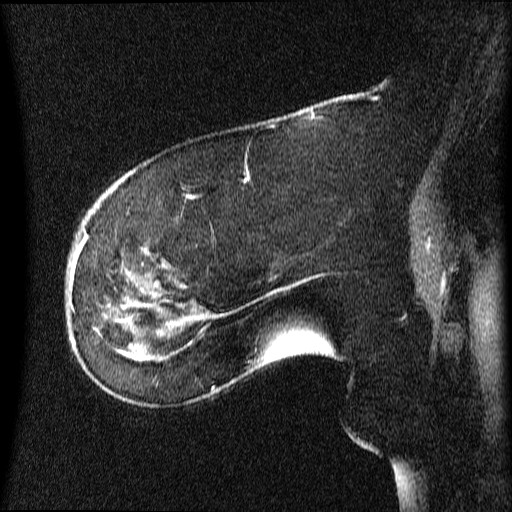
Breast MRI (dynamic contrast-enhanced), one sagittal slice; slice 21 of 64 in the series (ordered by position); dynamic contrast-enhanced series, image 2 of 4 at this slice position (ordered by acquisition); 1.5 T; TE 4.2 ms, TR 9 ms; 2 mm slice thickness; 512 × 512 image matrix, field of view 200 × 200 mm. Patient: female, 63 years.
Outlined on this slice (semi-automatically segmented with operator editing):
- analysis volume of interest (the breast-tissue region the enhancement analysis was run in; not a lesion): box from (x=68, y=272) to (x=131, y=353) px
- tumour enhancement mask (voxels above the 70 % enhancement threshold inside the analysis volume of interest): (x=71, y=272)–(x=126, y=353)